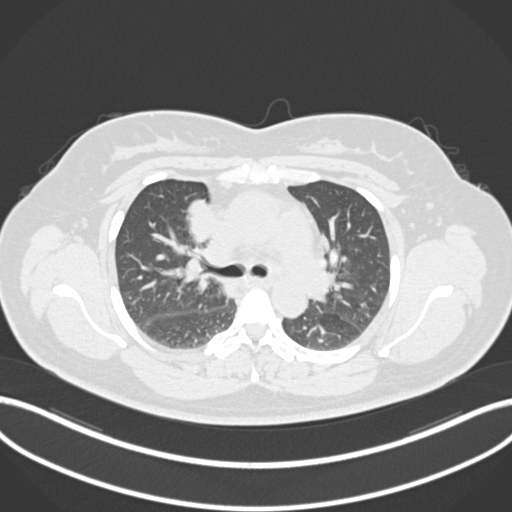
Chest CT, one axial slice; position 116 of 183 along the scan axis; reconstruction kernel B30f; 120 kVp; lung window (W 1500 / L -600 HU); 1 mm slice thickness; 512 × 512 image matrix, field of view 400 × 400 mm. Patient: female, 46 years. Case-level facts recorded for this patient, not image findings: clinical TNM (as recorded): T2a N1 M0.
Structures marked on this image (rectangle marked by the reading radiologist):
- lung tumour (recorded histology: adenocarcinoma): box from (x=185, y=195) to (x=213, y=243) px